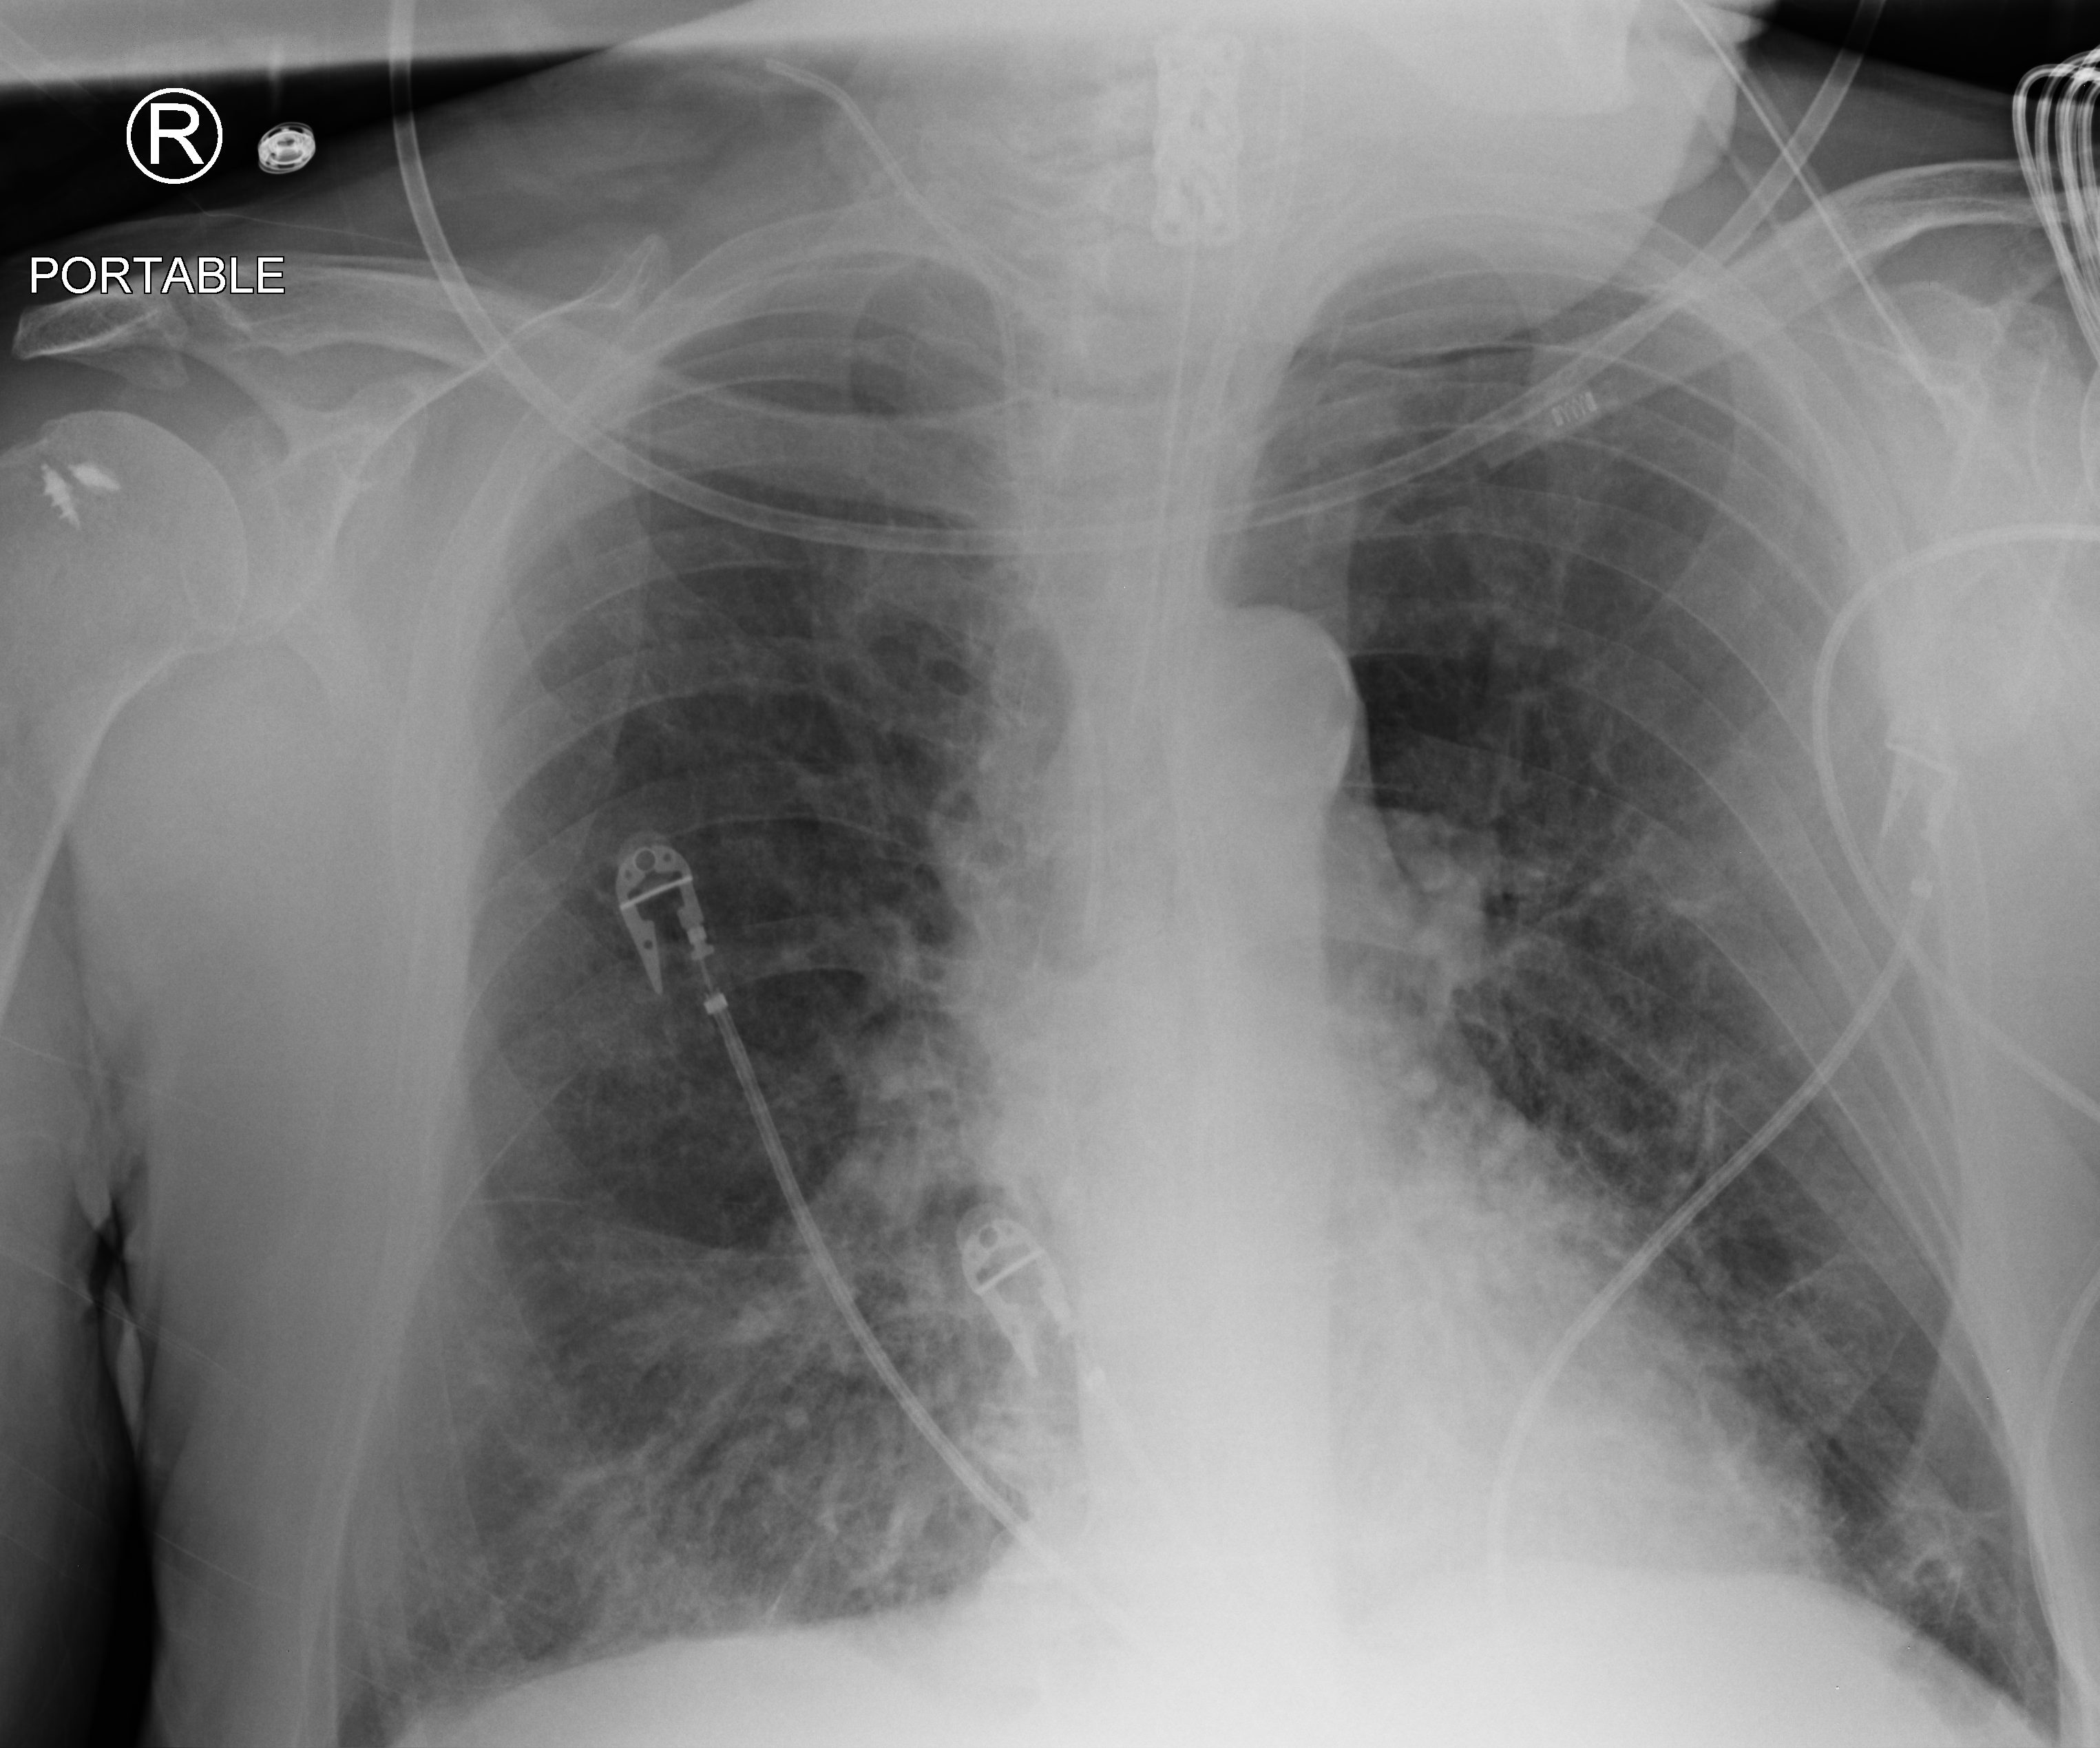
Portable chest radiograph, anteroposterior (AP) projection. Patient hospitalised with COVID-19; male, aged 75–90 years.
Hospital-stay facts (about this admission, not read from this image; timing relative to this image not recorded): length of hospital stay: 26 days.